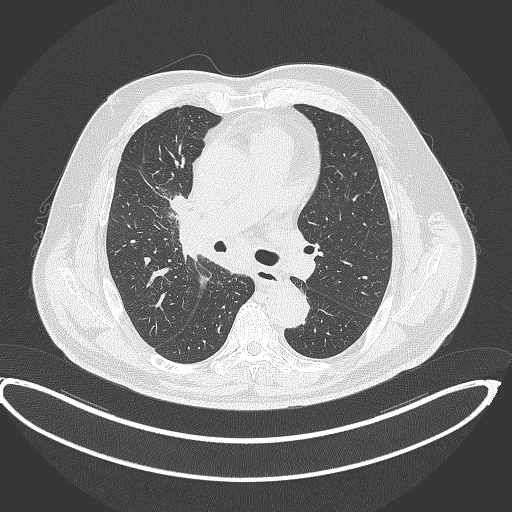
Chest CT, one axial slice; position 244 of 390 along the scan axis; reconstruction kernel B70f; lung window (W 1500 / L -600 HU); 1 mm slice thickness; 512 × 512 image matrix, field of view 448 × 448 mm. Patient: male, 62 years. From the clinical record (not read from this slice): clinical TNM (as recorded): T1c N3 M1c.
Structures marked on this image (rectangle marked by the reading radiologist):
- lung tumour (recorded histology: adenocarcinoma): bounding box <165,192,192,218> (left, top, right, bottom; pixels)